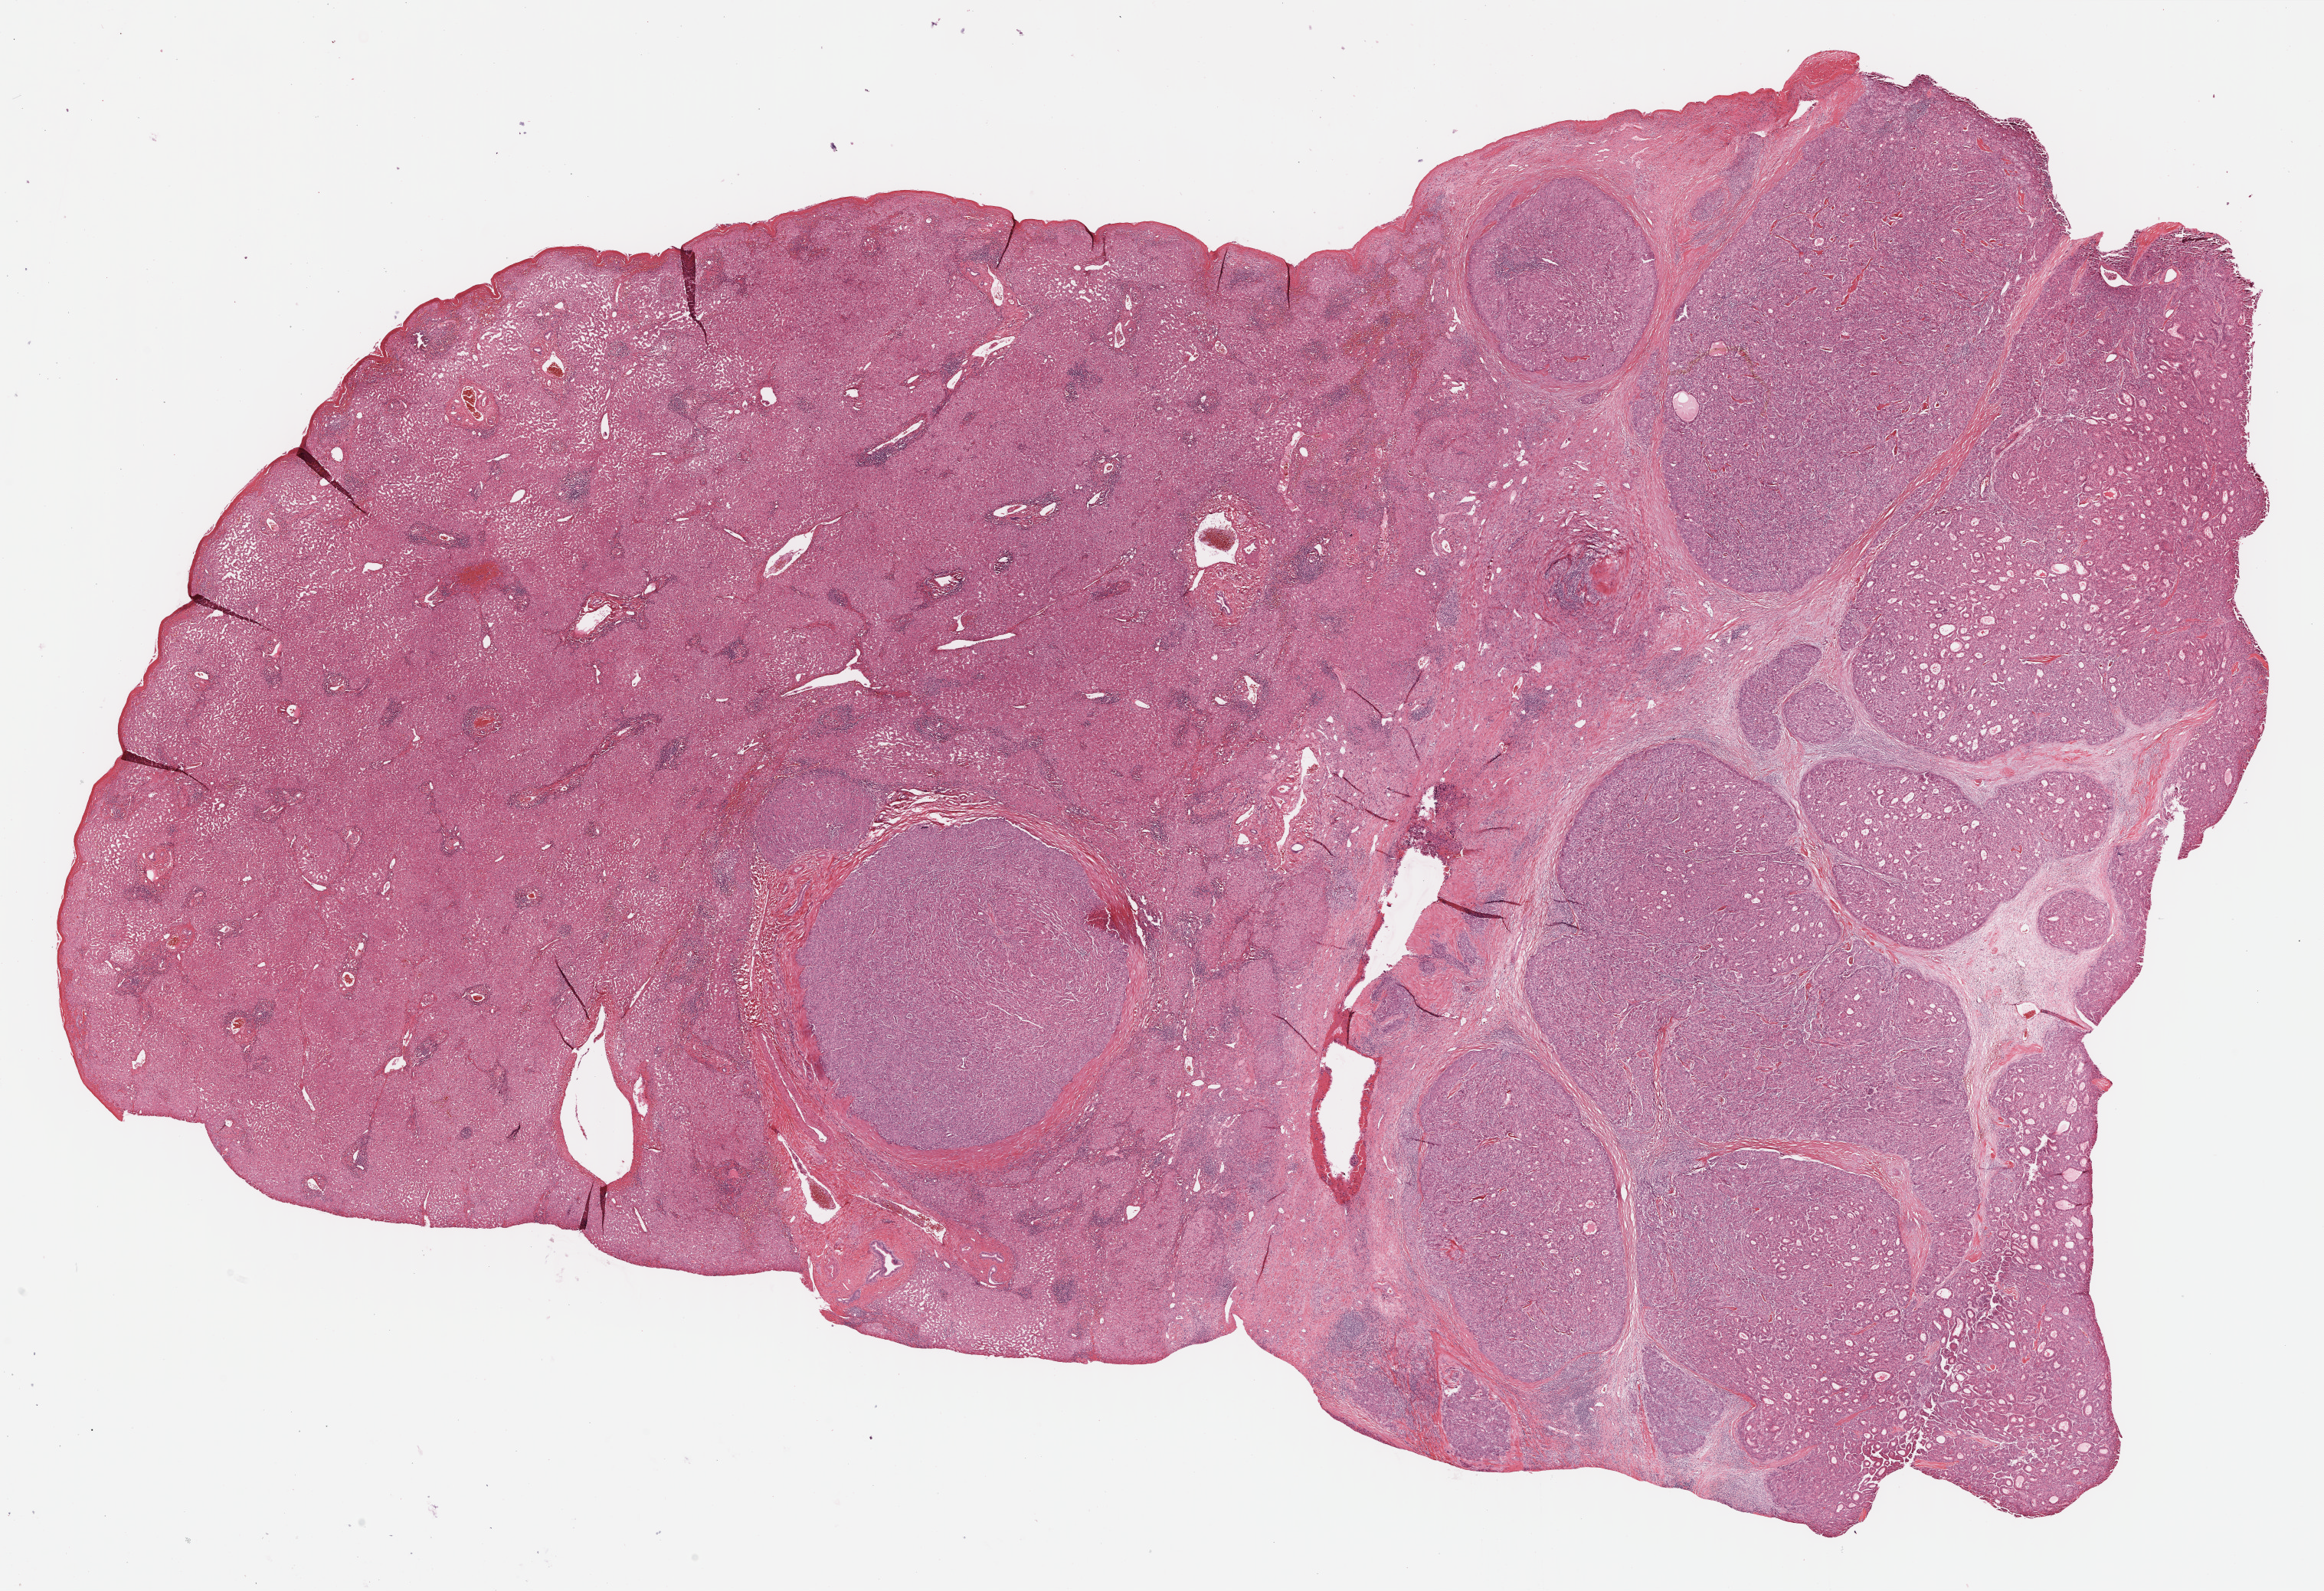
Hematoxylin and eosin (H&E) stained whole-slide image, whole scanned area (about 24.6 x 16.8 mm) shown as a low-resolution overview. Formalin-fixed paraffin-embedded (FFPE) diagnostic section. Sample: primary tumour, liver. Male patient; age at initial diagnosis 77 years. Histologic grade: G3 (poorly differentiated).
AJCC pathologic stage: II (5th edition). Histologic diagnosis: Hepatocellular carcinoma, NOS.